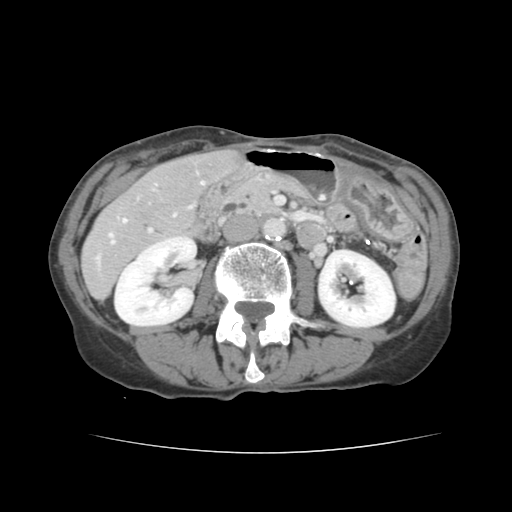
Contrast-enhanced abdominal CT, one axial slice. Position 53 of 136 along the scan axis. Intravenous contrast given. Soft-tissue window (W 400 / L 40 HU). 2.5 mm slice thickness. 512 × 512 image matrix, field of view 319 × 319 mm. Female patient, age 77 years. Case-level facts recorded for this patient, not image findings: diagnosis: colorectal cancer liver metastases, imaged before liver resection; multiple liver metastases: yes; largest metastasis: 3 cm; disease in both lobes: no.
Annotated regions visible in this slice (expert manual segmentation):
- hepatic veins: bounding box <109,181,204,244> (left, top, right, bottom; pixels)
- liver: <83,150,237,299>
- planned liver remnant (the part of the liver to remain after resection): <168,151,237,194>
- portal vein (with intrahepatic branches): <148,229,152,232>